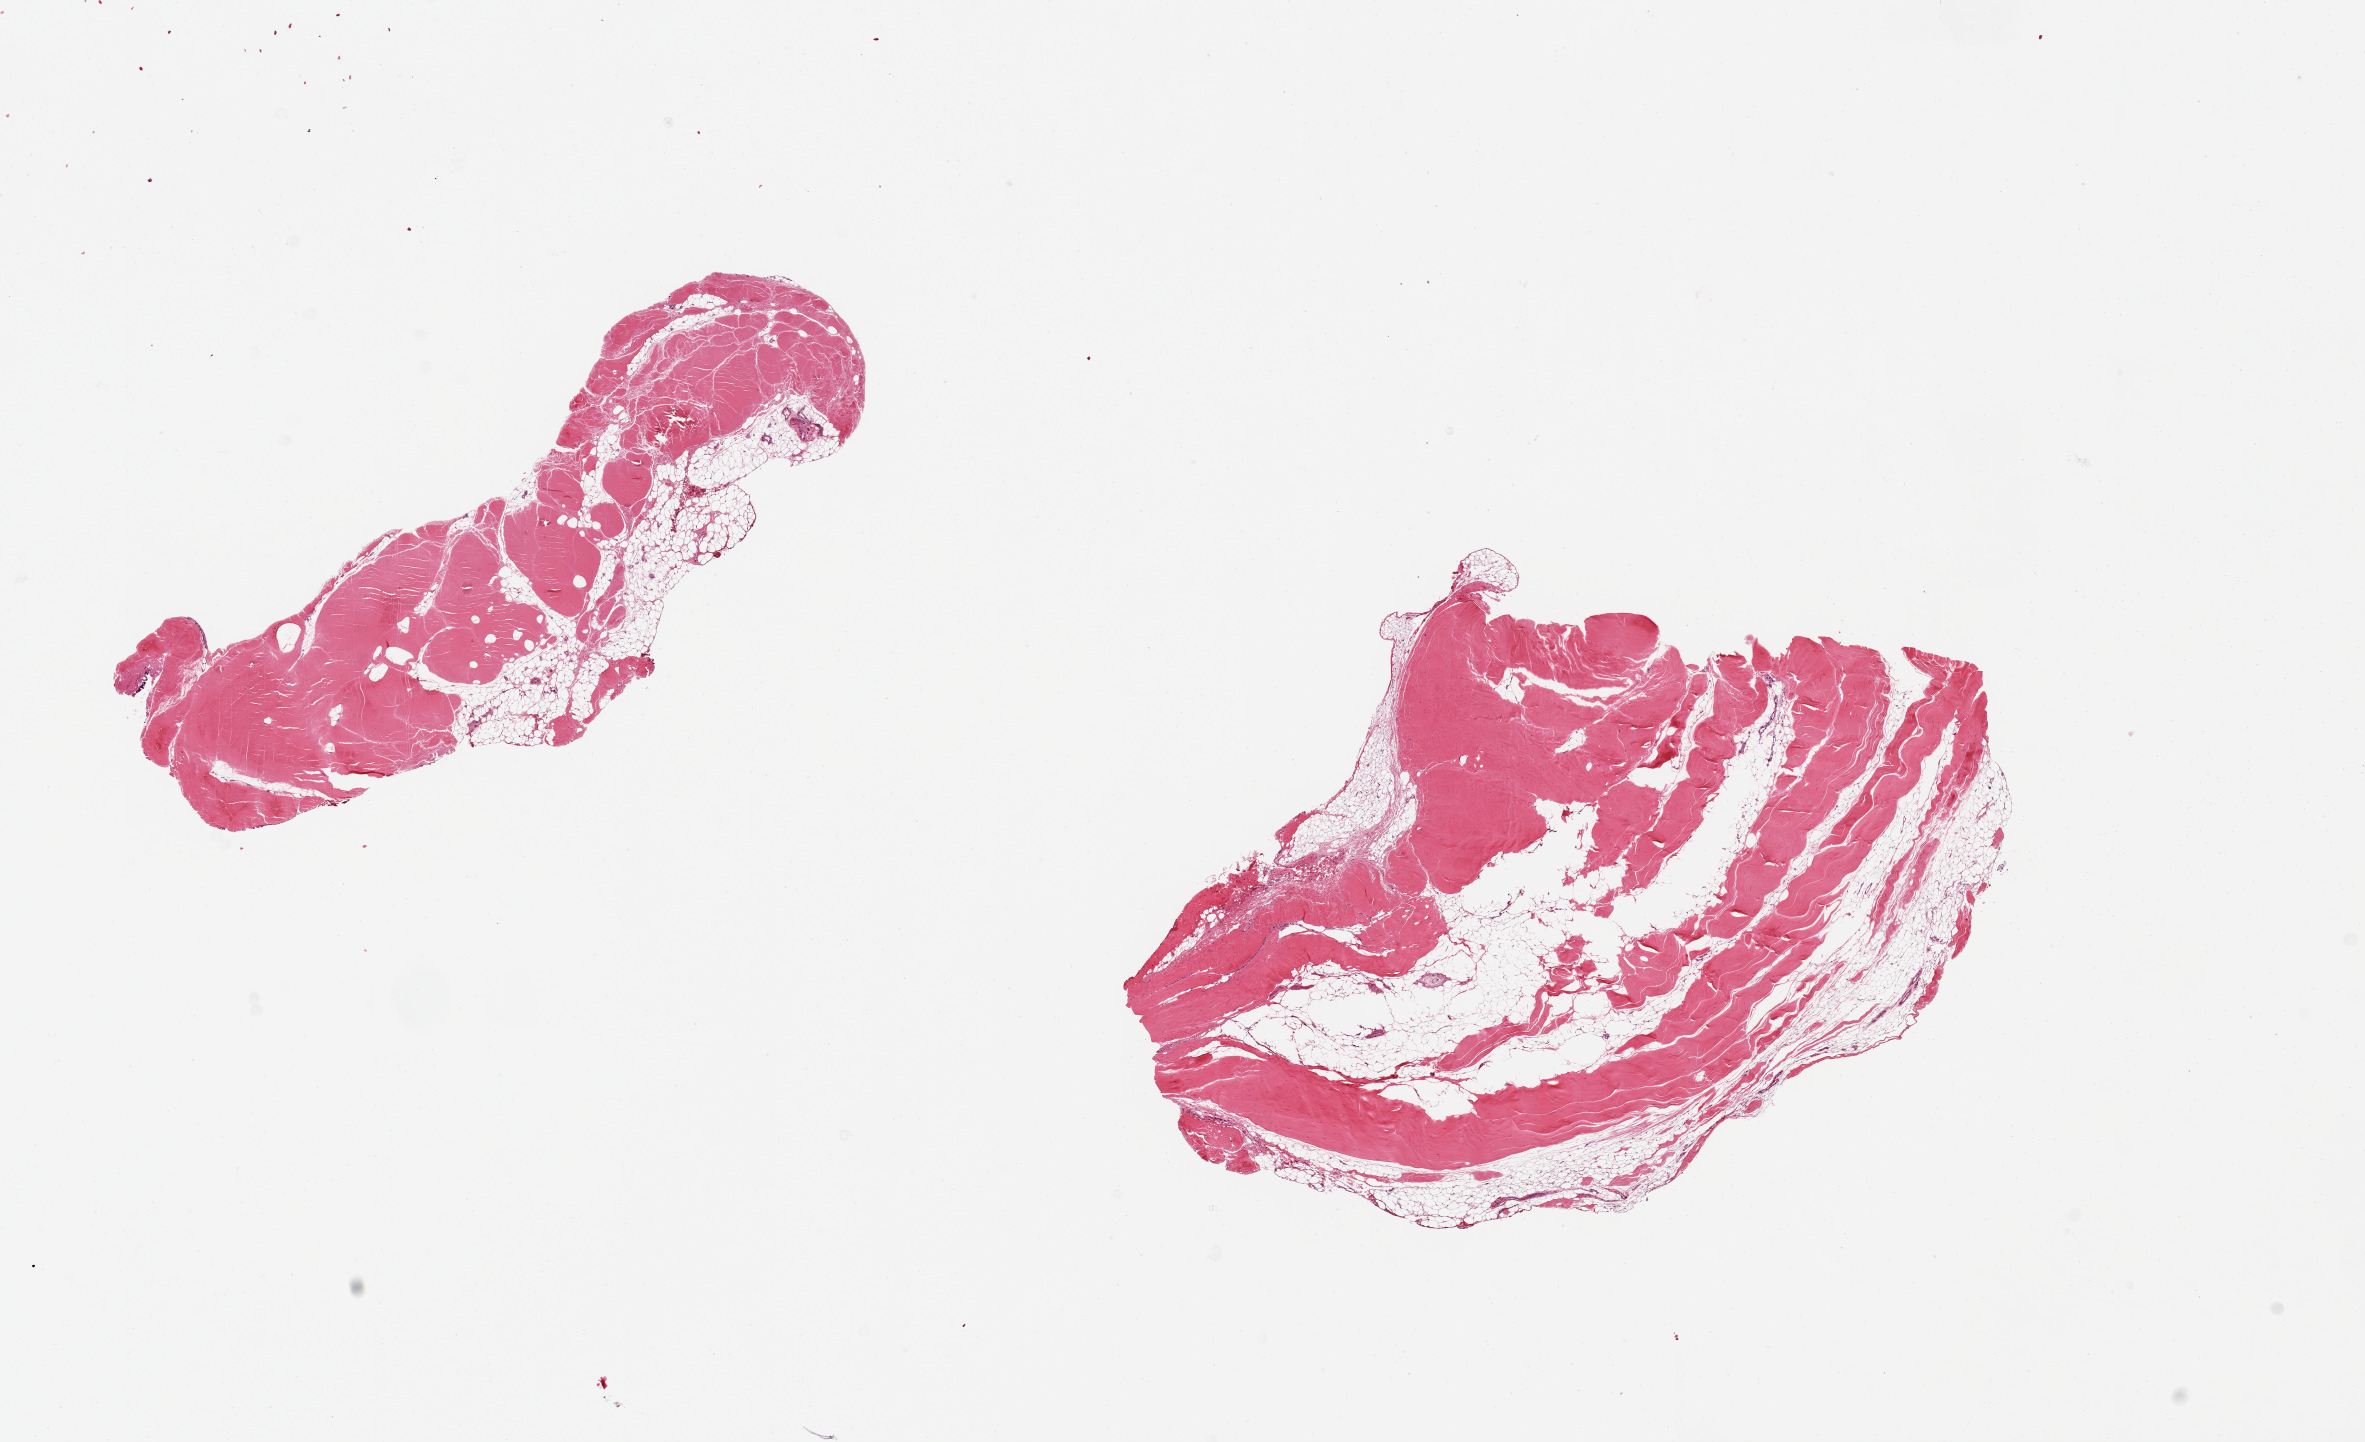
Digitized haematoxylin and eosin-stained section, a low-resolution overview of the entire scanned area, about 18.7 x 11.4 mm; PAXgene-fixed, paraffin-embedded tissue; target tissue: tibial nerve; tissue donor sample. Male donor.
- review note (as recorded): 2 pieces, 6x3 & 7x5mm; NO NERVE. Tendon: dense fibrous and adipose tissue